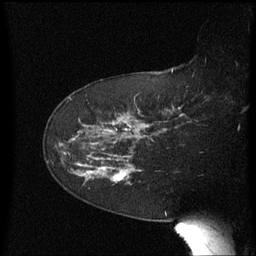
Breast MRI (dynamic contrast-enhanced), one sagittal slice; slice 41 of 60 in the series (ordered by position); dynamic contrast-enhanced series, image 2 of 3 at this slice position (ordered by acquisition); 1.5 T; TE 4.2 ms, TR 8.4 ms; 256 × 256 image matrix, field of view 200 × 200 mm. Female patient, age 63 years. From the clinical record (not read from this slice): setting: breast cancer imaged before/during neoadjuvant chemotherapy; receptor status: HER2-positive.
Annotated regions visible in this slice (semi-automatic segmentation, software-assisted and operator-edited):
- analysis volume of interest (the breast-tissue region the enhancement analysis was run in; not a lesion): bounding box [x1, y1, x2, y2] px = [66, 136, 138, 185]
- tumour enhancement mask (voxels above the 70 % enhancement threshold inside the analysis volume of interest): [114, 170, 127, 181]